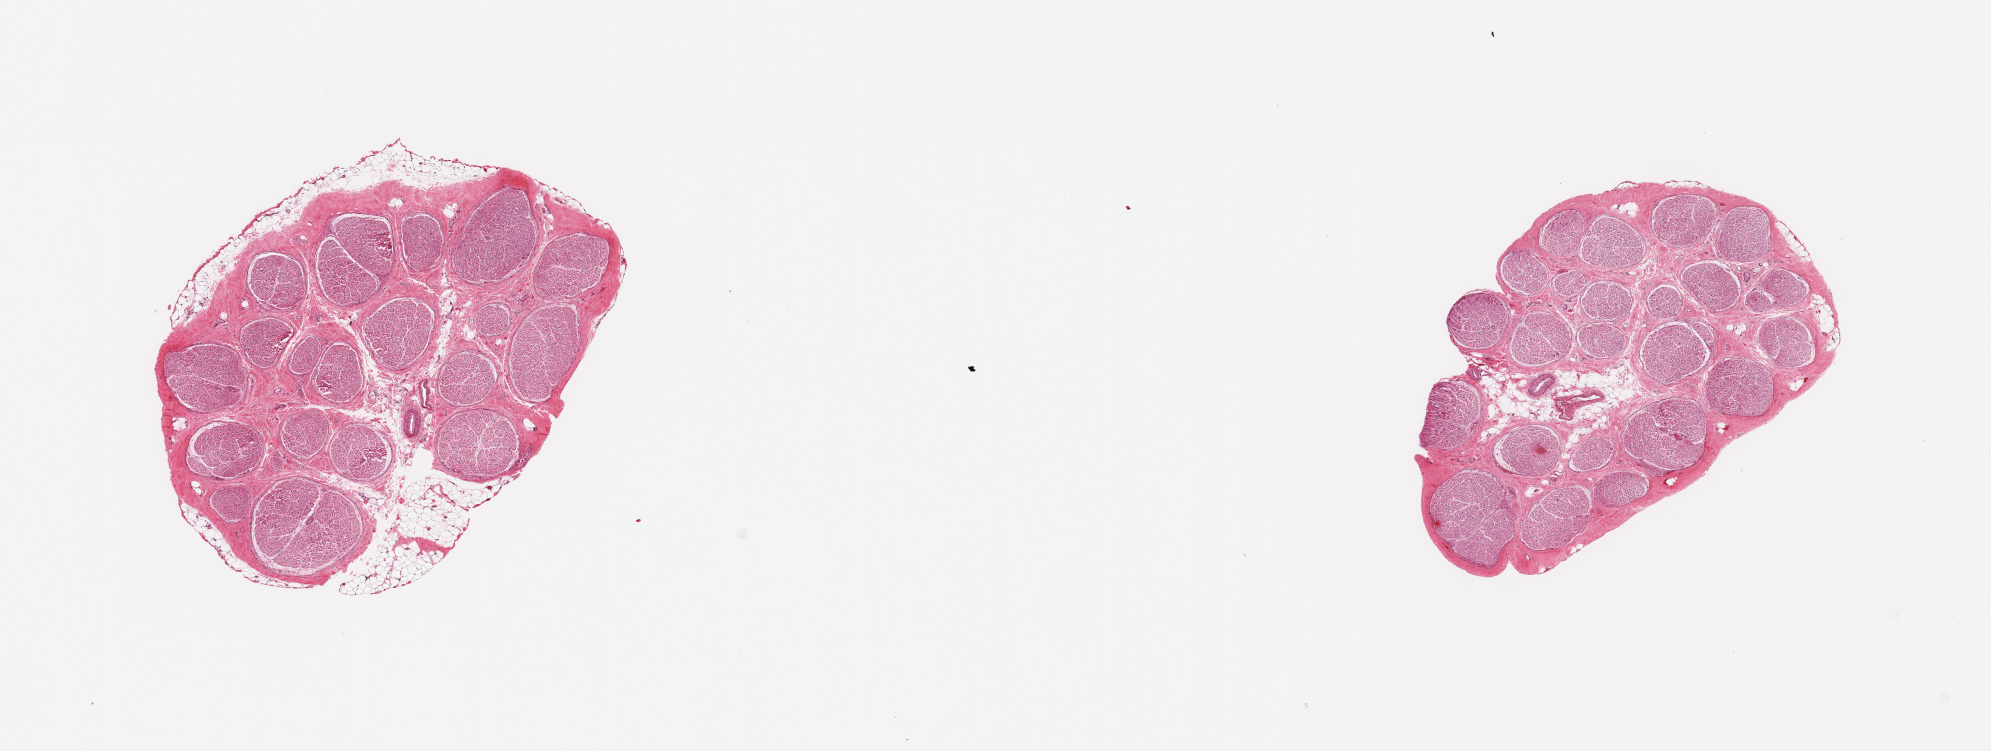
Whole-slide image, hematoxylin and eosin (H&E) stain, brightfield — shown as a low-resolution overview of the whole scanned area (about 15.8 x 5.9 mm, slide scanned at 20x). PAXgene-fixed paraffin-embedded (PFPE) section. Sampled site (target tissue): tibial nerve. Donor tissue sample. Male donor.
- reviewer comment on this tissue sample: 2 pieces; 1 piece has small partial rim of fat